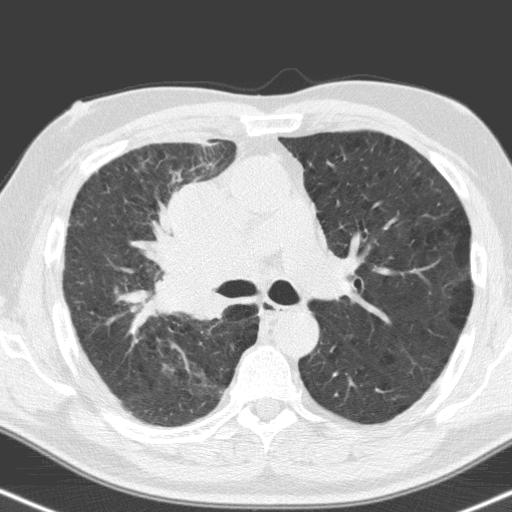
Low-dose screening chest CT, one axial slice; position 104 of 160 along the scan axis; 120 kVp; lung window (W 1500 / L -600 HU); 3.2 mm slice thickness; 512 × 512 image matrix, field of view 324 × 324 mm.
Annotated regions visible in this slice (outlined manually by an expert reader):
- lesion 1 (tumor, hilum of right lung): bounding box [x1, y1, x2, y2] px = [158, 183, 263, 319]